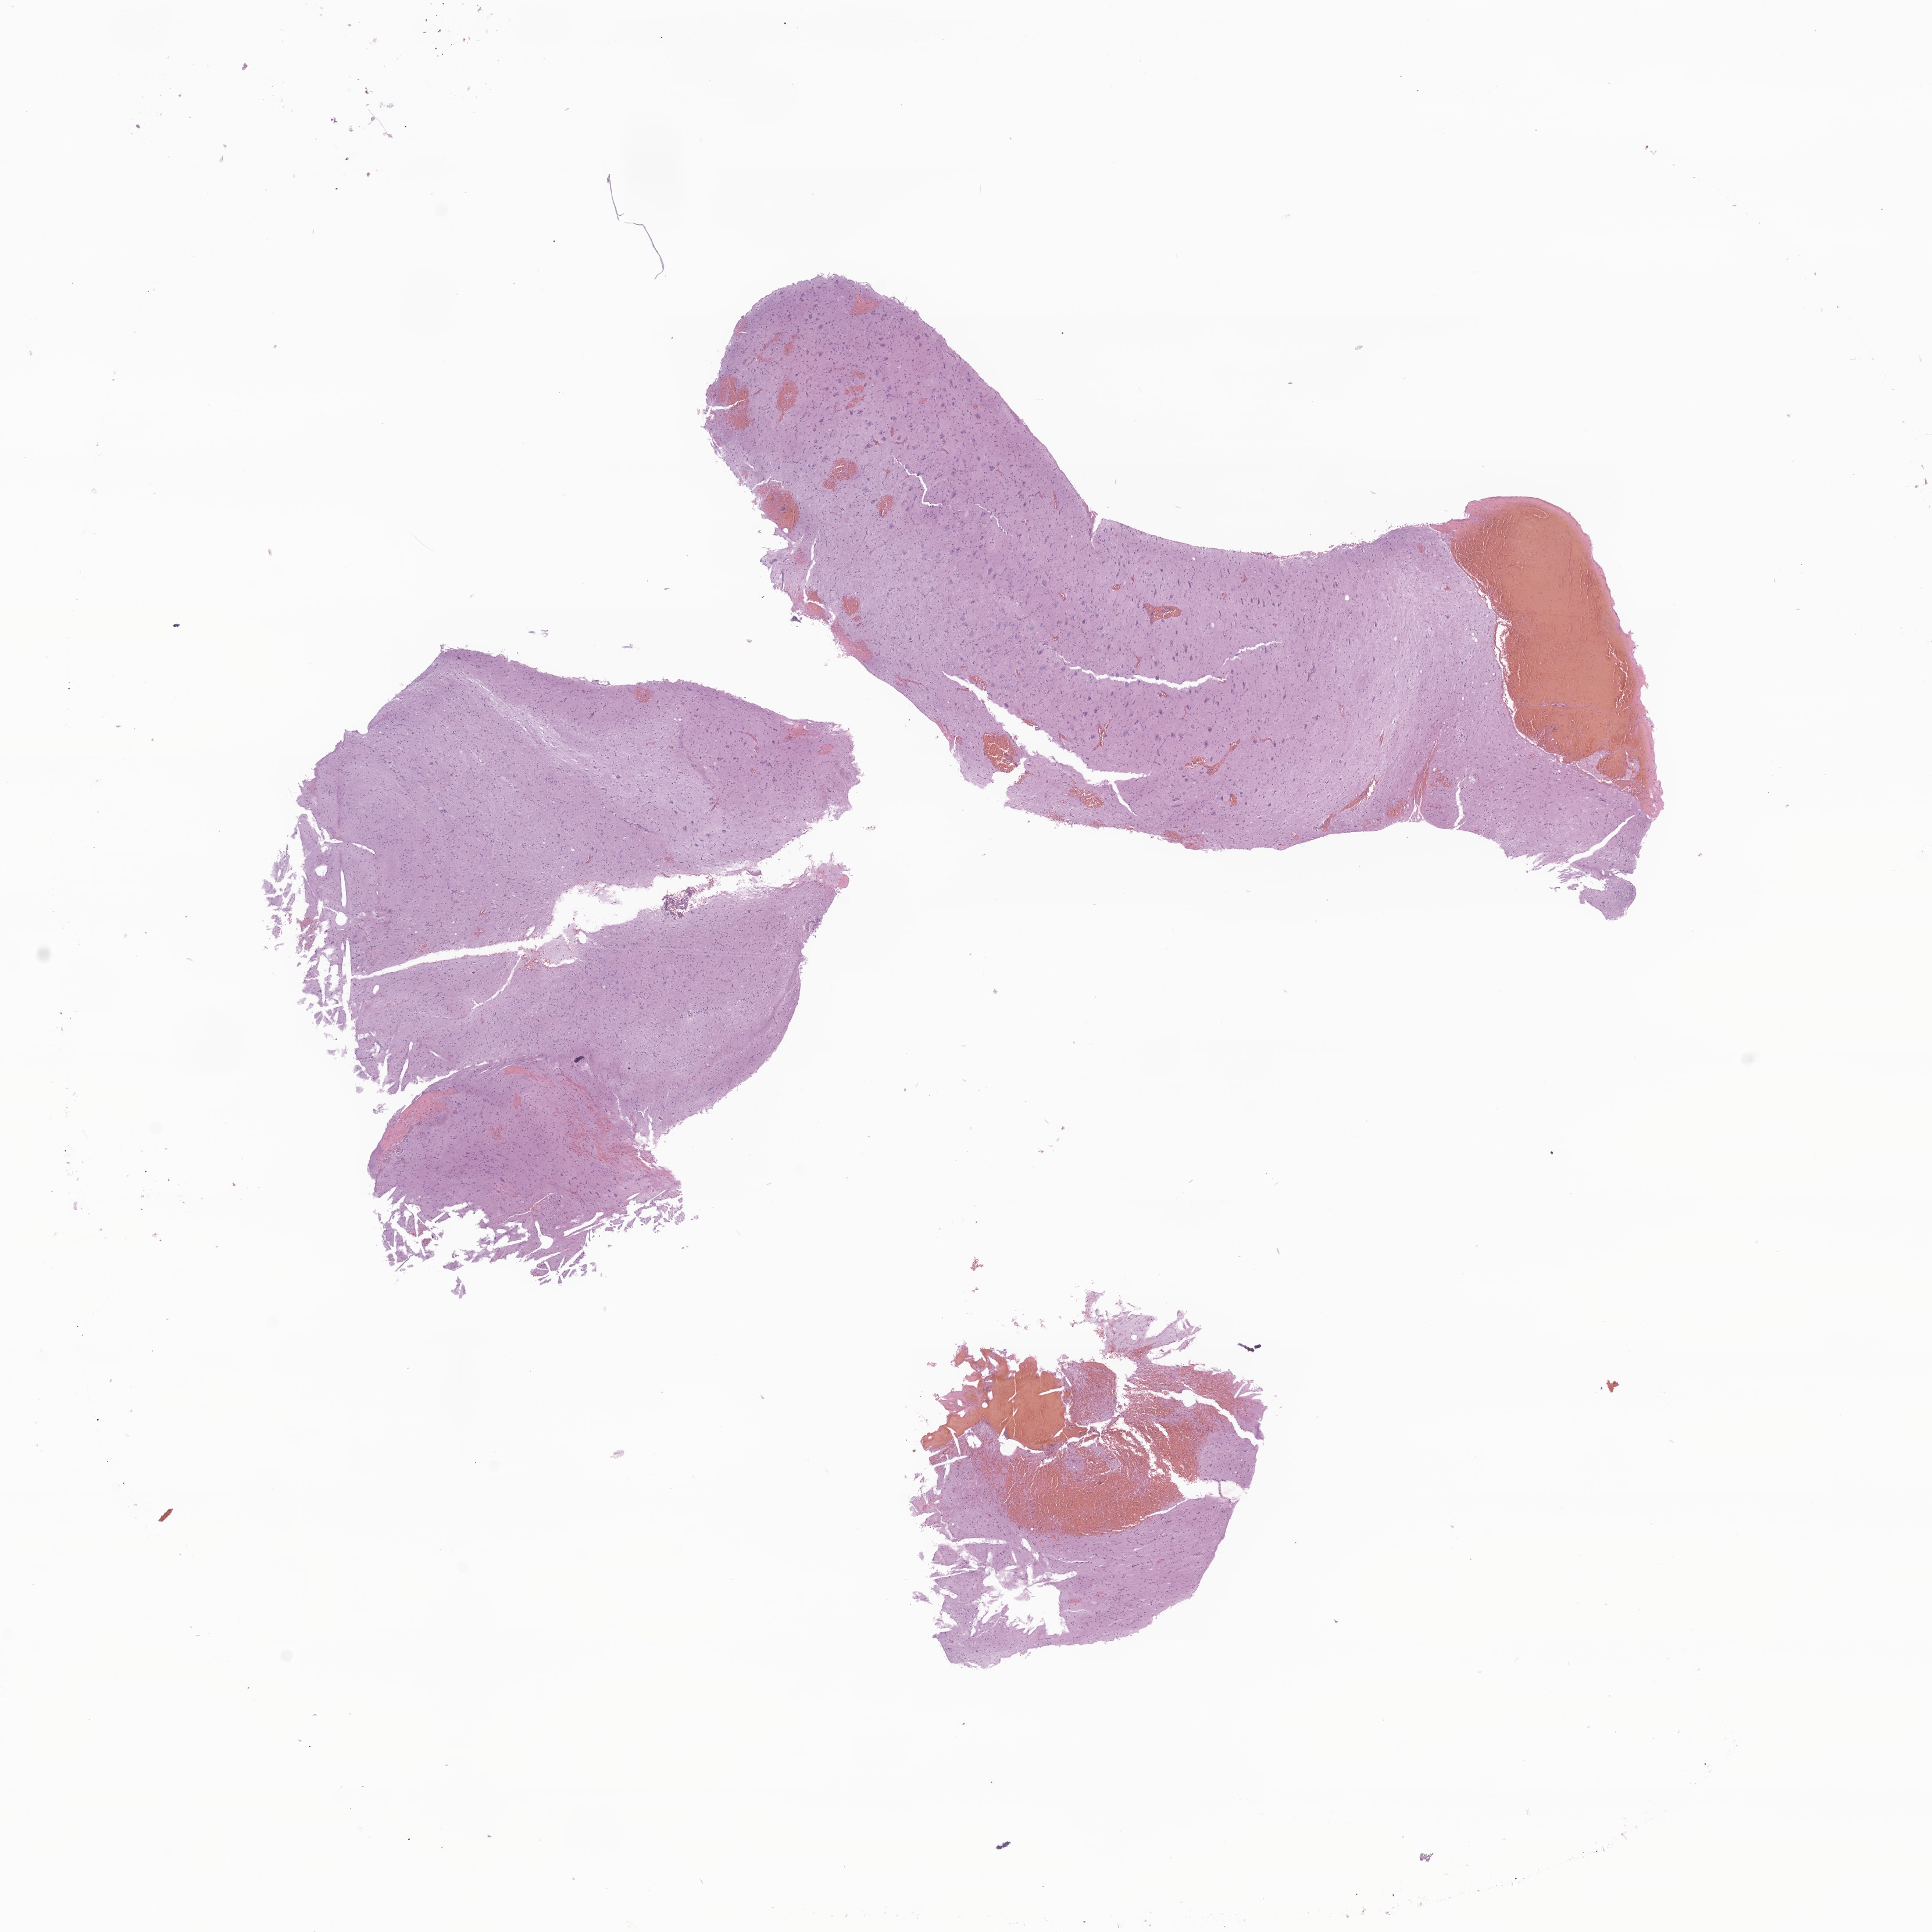
Digitized H&E-stained section of tumor tissue from the brain stem — a low-resolution overview of the entire scanned area, about 14.0 x 14.0 mm, formalin-fixed, paraffin-embedded (FFPE) tissue. Patient: female, age 222 months (18 years 6 months).
Diagnosis (ICD-O-3 morphology term): Pilocytic astrocytoma.